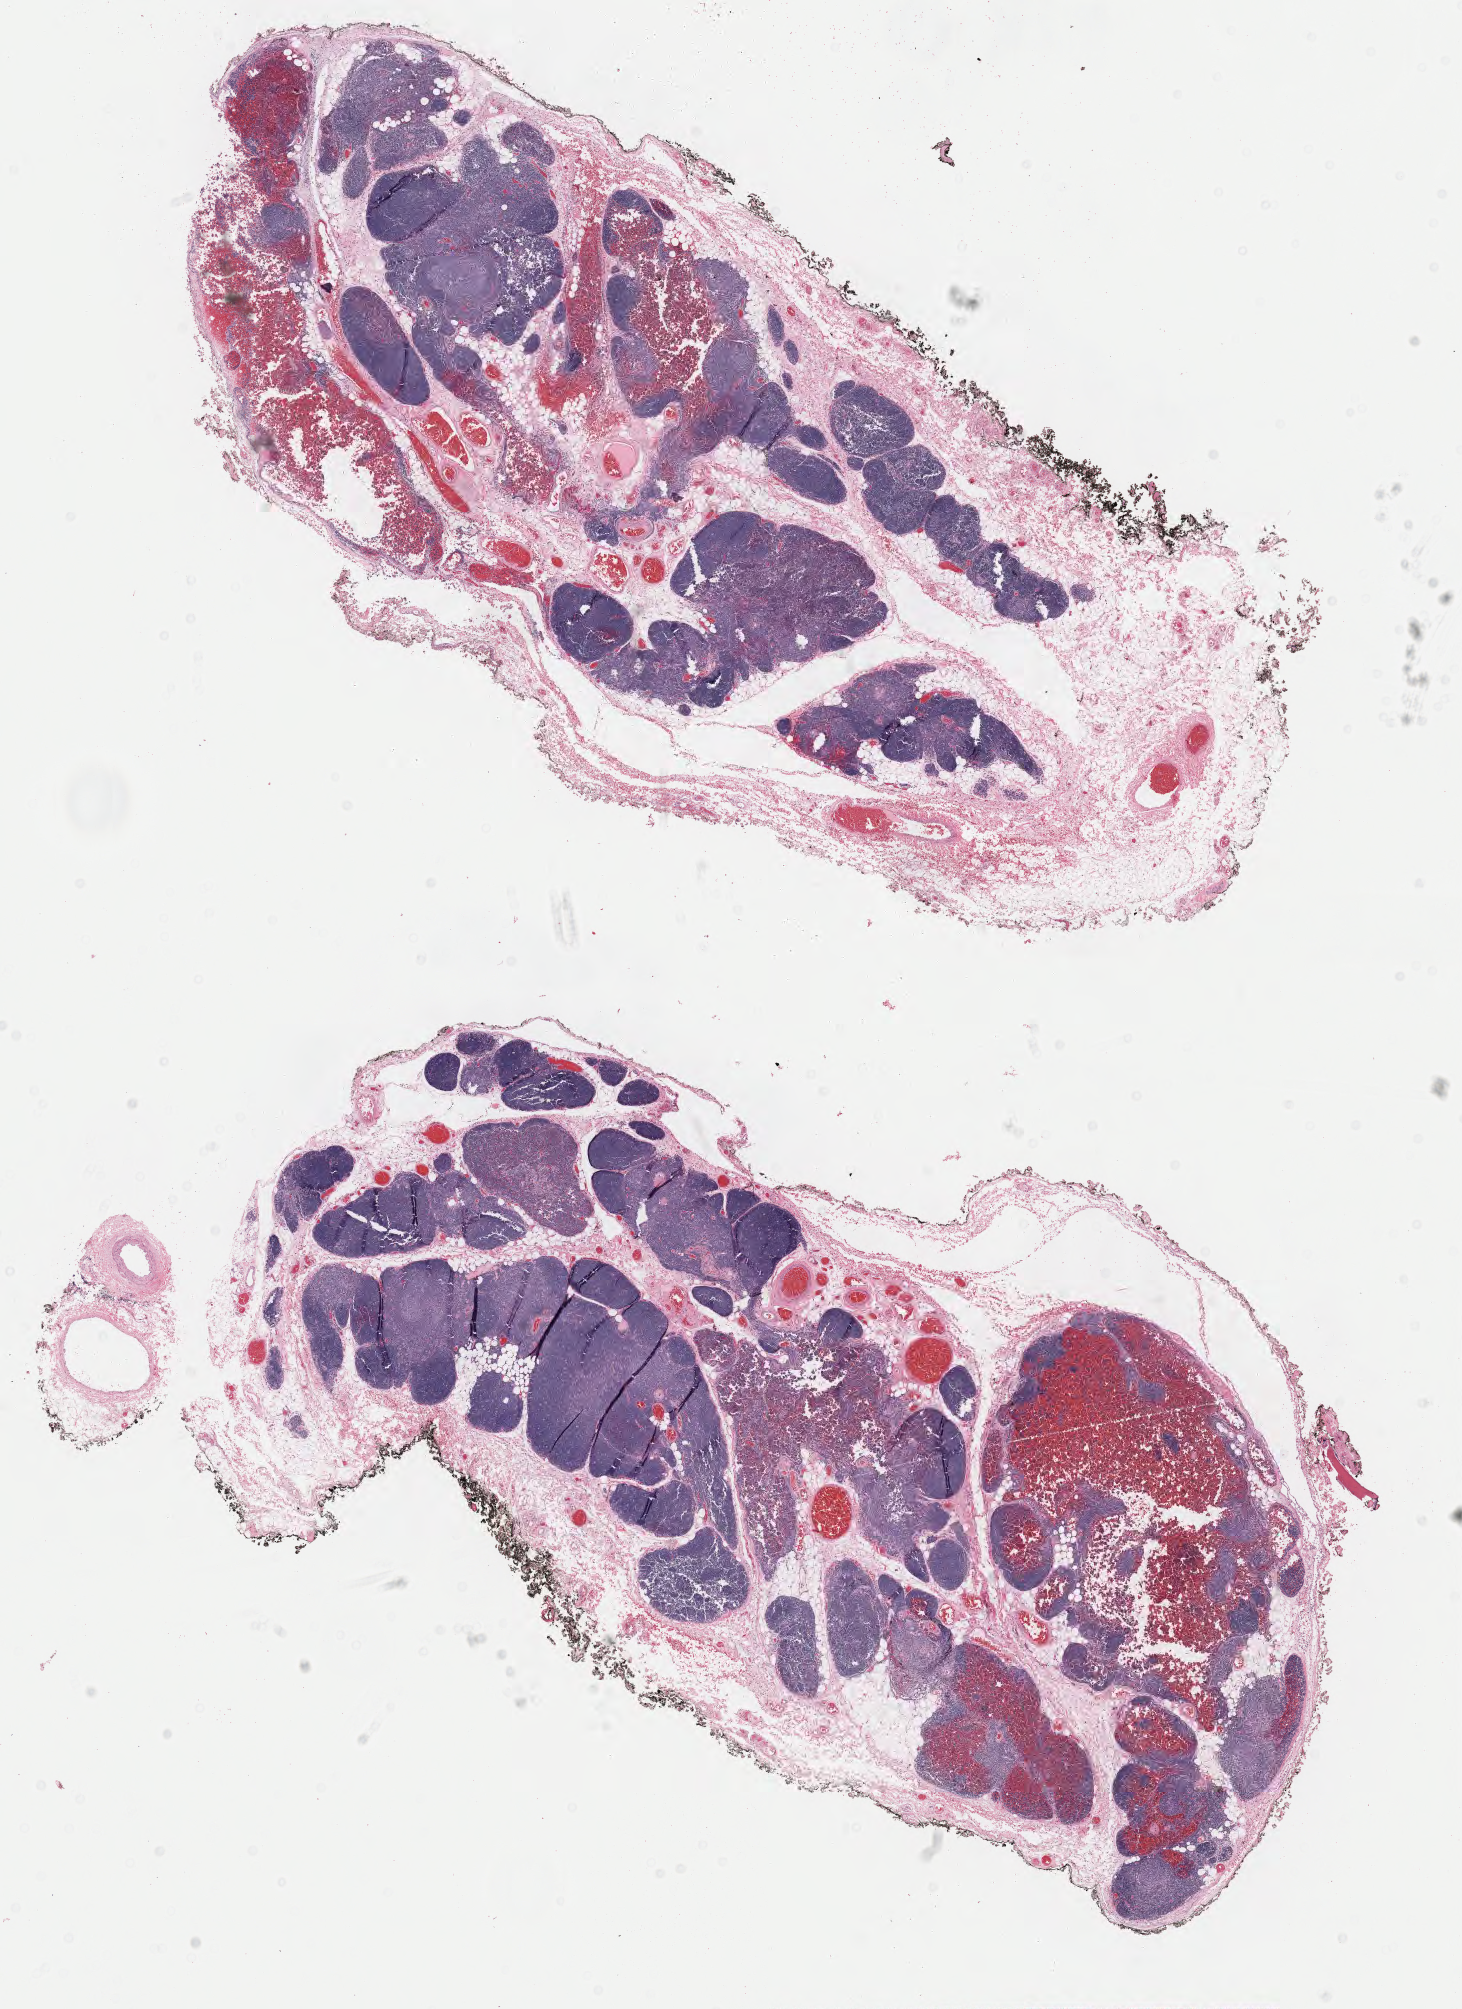
Whole-slide histology image, H&E-stained — a low-resolution overview of the entire scanned area, about 11.6 x 15.9 mm (slide scanned at 40x); formalin-fixed paraffin-embedded (FFPE) diagnostic section; thymus, primary tumour sample. Patient: female, age at initial diagnosis 43 years.
* pathologic diagnosis: Thymoma, type B2, malignant